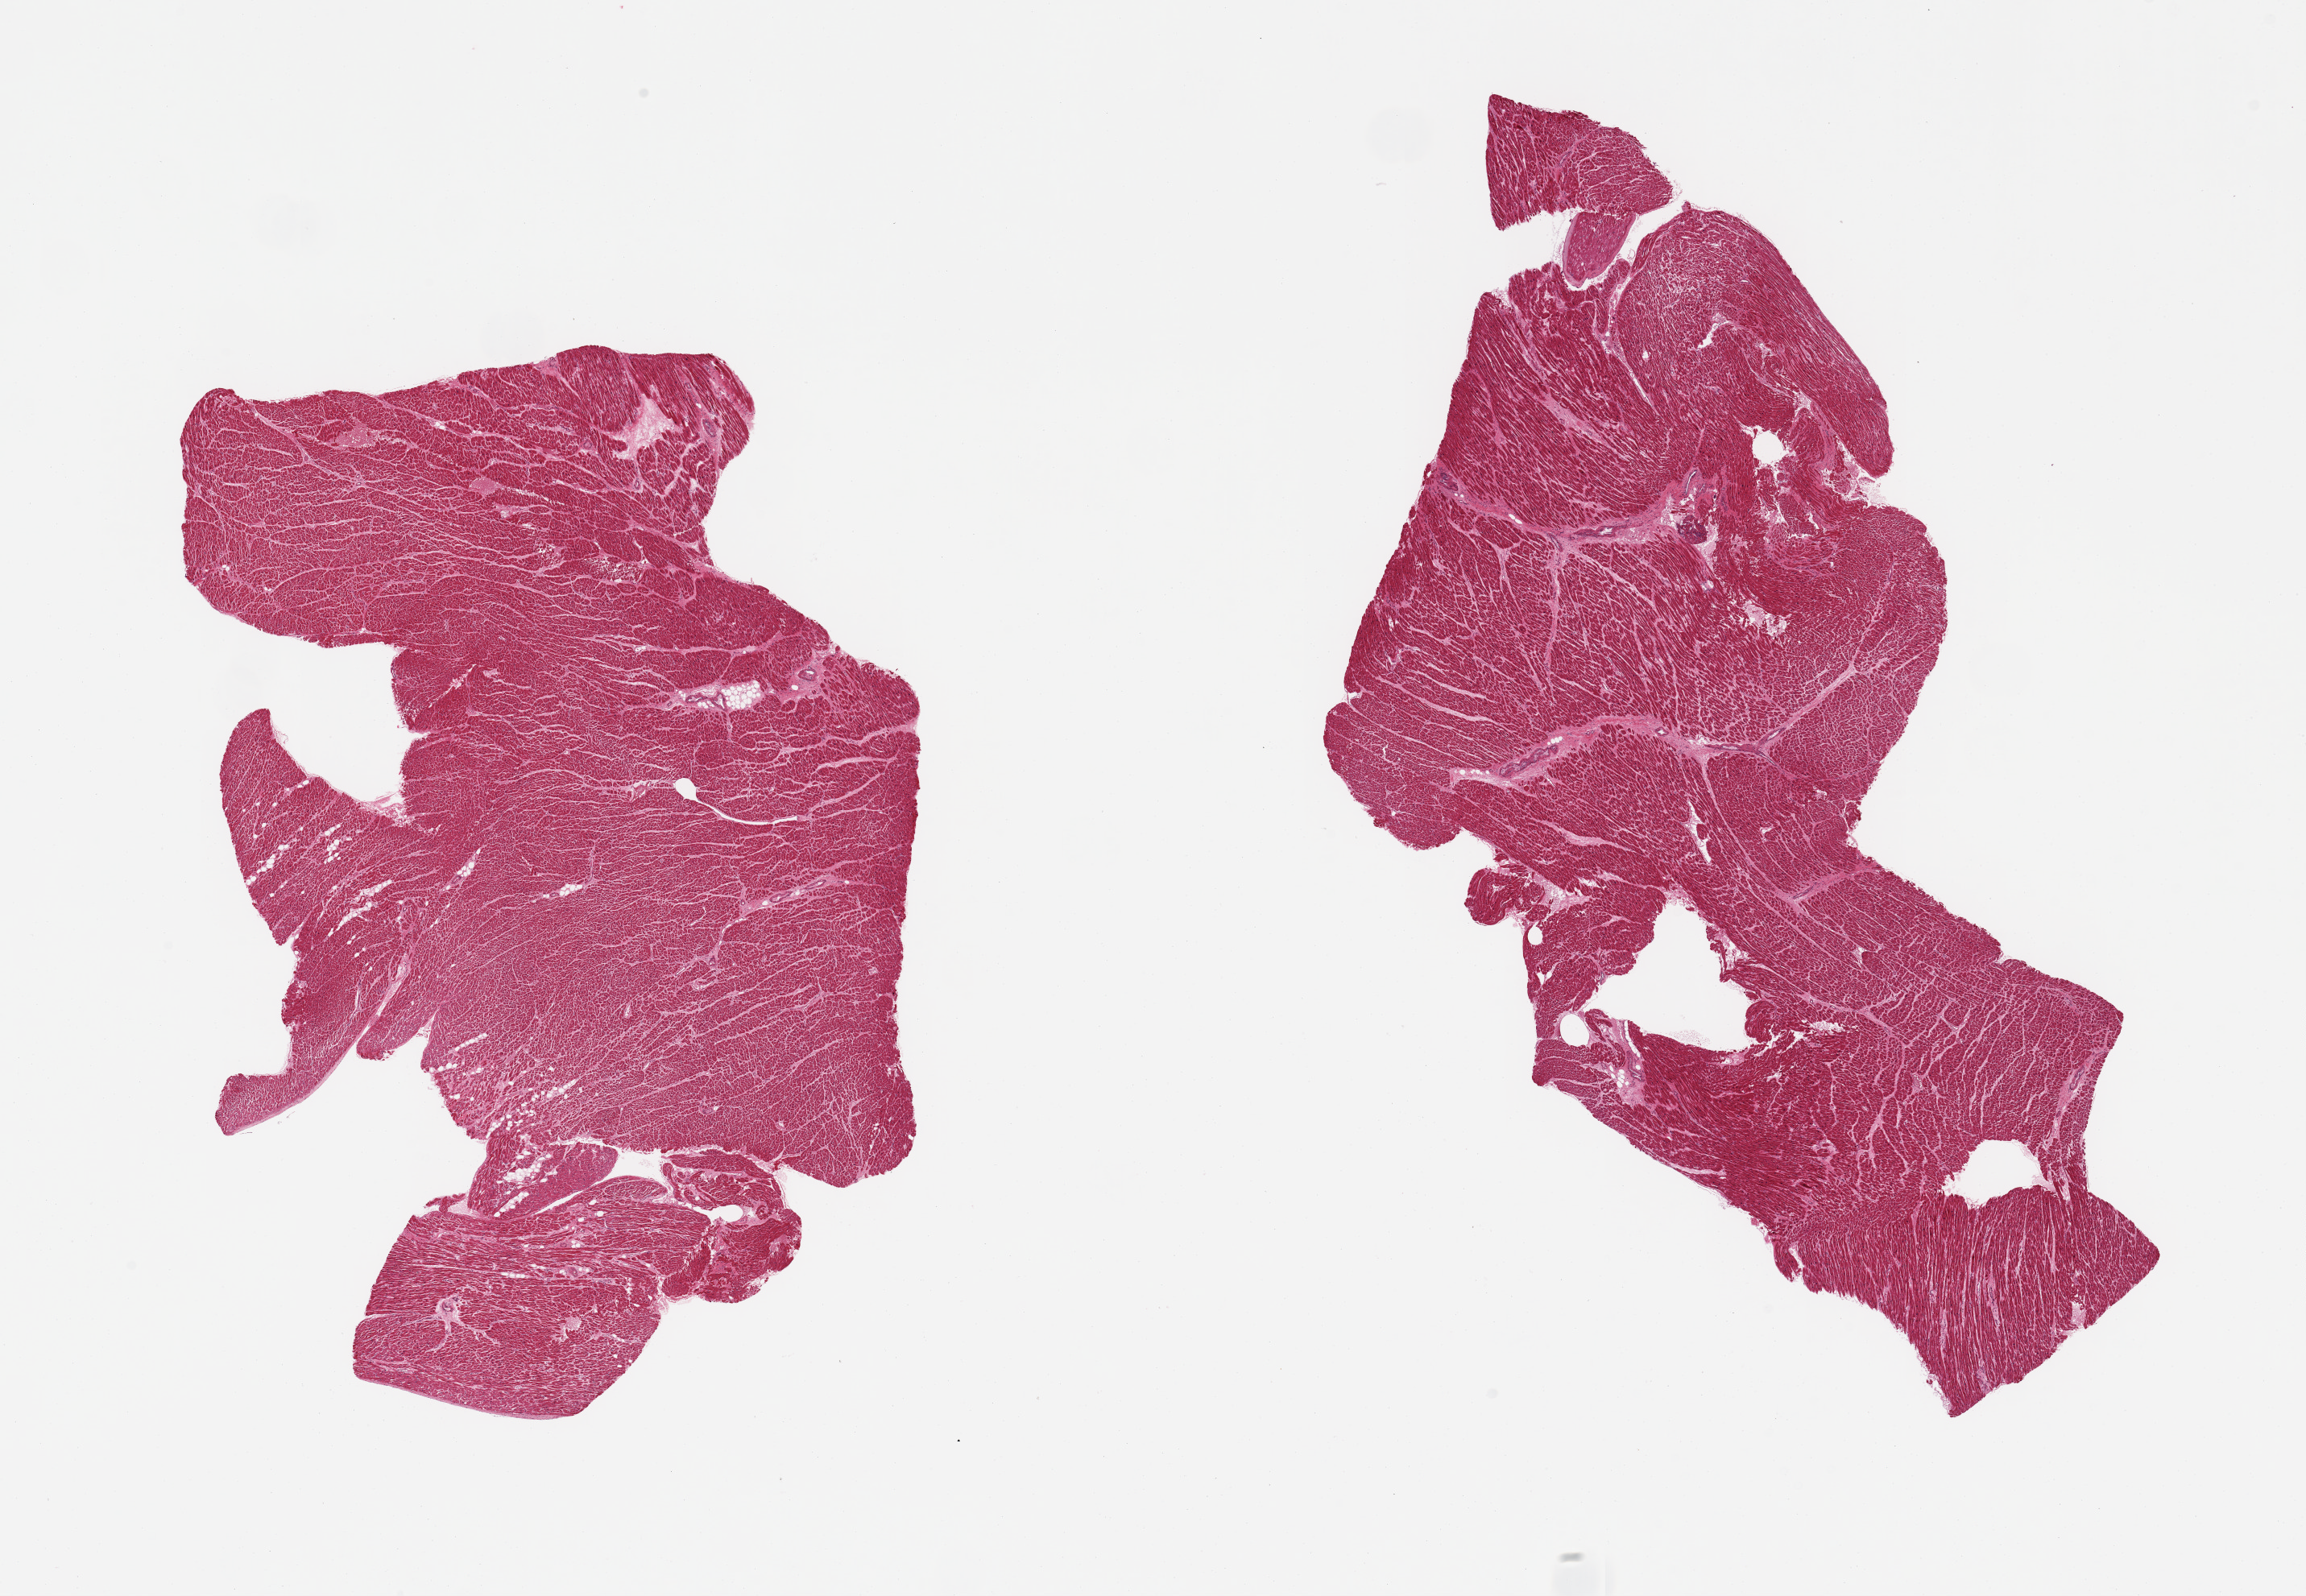
Whole-slide image, H&E stain, brightfield — low-resolution overview of the scanned area, about 22.6 x 15.7 mm (acquisition: 20x scan); PAXgene-fixed paraffin-embedded (PFPE) section; sampled site (target tissue): heart; tissue donor sample. Donor sex: female.
• review note (as recorded): 2 pieces; some interstitial fibrosis and myocyte hypertrophy